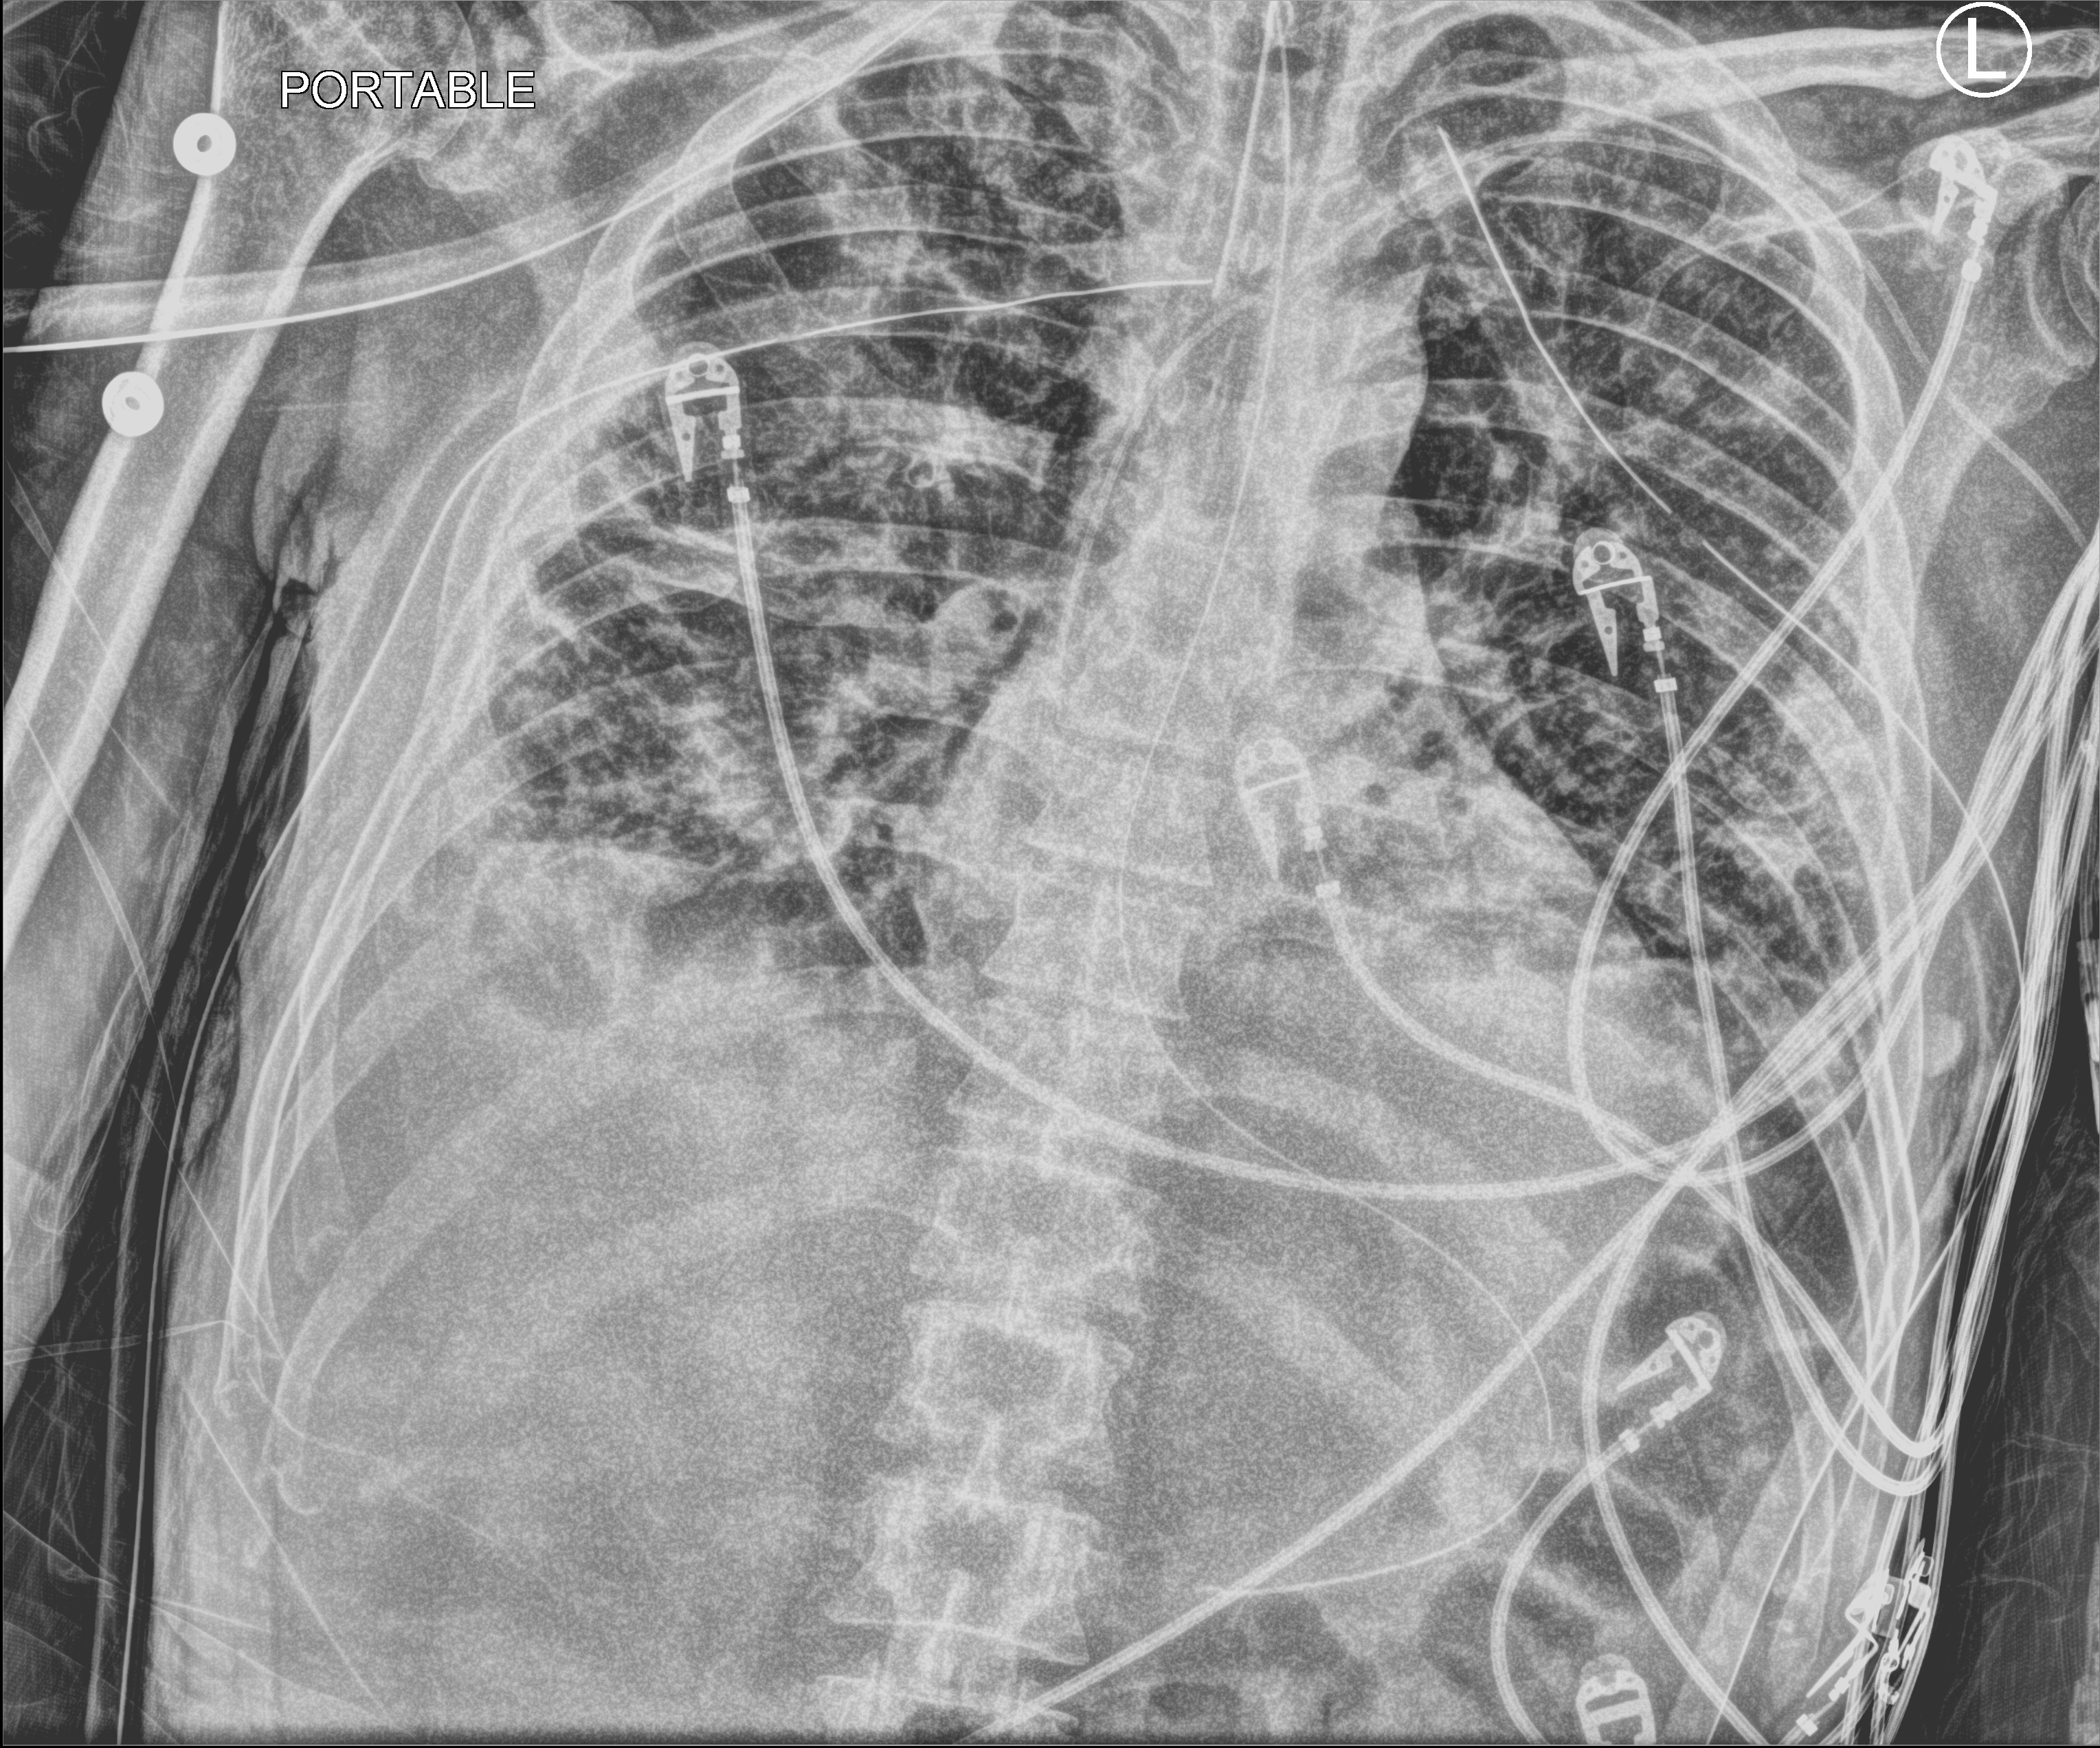
Portable chest radiograph, anteroposterior (AP) projection. Male patient hospitalised with COVID-19, age 18–59 years.
From the hospital-stay record, not from the radiograph (when in the stay this image was taken is not recorded):
- smoking status (admission record): never